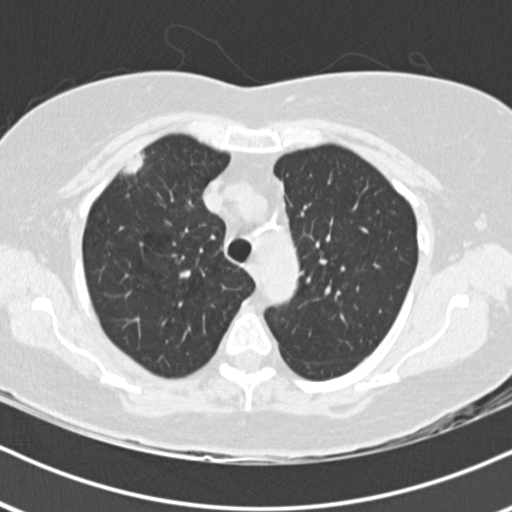
Low-dose screening chest CT, one axial slice; slice 138 of 178 in the series (ordered by position); reconstruction kernel B30f; lung window (W 1500 / L -600 HU); 512 × 512 image matrix.
Outlined on this slice (manually delineated by an expert):
- lesion 1 (tumor, upper lobe of right lung): box from (x=123, y=153) to (x=145, y=175) px